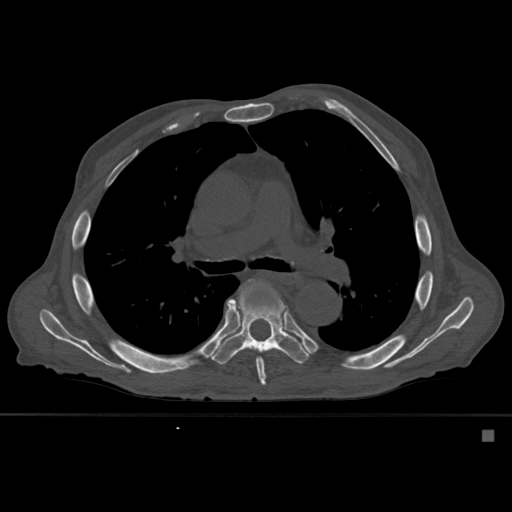
CT including the spine, one axial slice; slice 374 of 527 in the series (ordered by position); bone window (W 1800 / L 400 HU); 1.5 mm slice thickness; 512 × 512 image matrix. Male patient, age 78 years. Case-level facts recorded for this patient, not image findings: primary cancer: prostate.
Structures marked on this image (semi-automatic segmentation, software-assisted and operator-edited):
- T6 vertebra: bounding box <230,279,278,386> (left, top, right, bottom; pixels)
- T7 vertebra: <212,283,310,365>